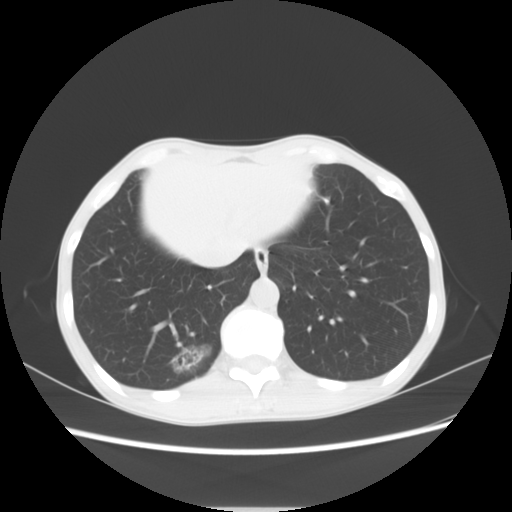
Chest CT, one axial slice. Slice 18 of 69 in the series (ordered by position). Reconstruction kernel STANDARD. Lung window (W 1500 / L -600 HU). 5 mm slice thickness. 512 × 512 image matrix. Female patient, age 51 years. Case-level facts recorded for this patient, not image findings: clinical TNM (as recorded): T1c N0 M0; histopathological grade: G2-3.
Annotated regions visible in this slice (bounding box drawn by a radiologist):
- lung tumour (recorded histology: adenocarcinoma): bounding box (x1, y1, x2, y2) in pixels: (153, 334, 210, 383)